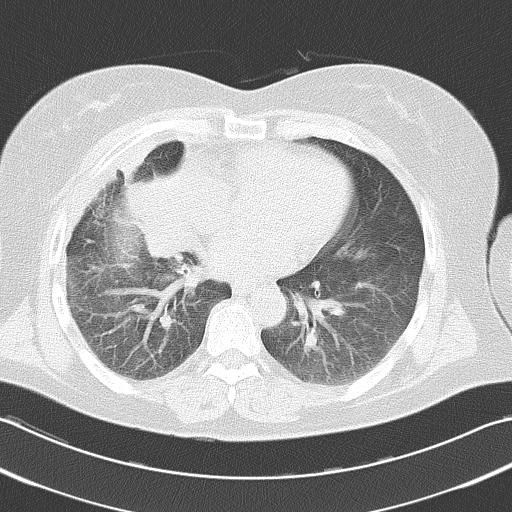
Chest CT, one axial slice. Slice 13 of 38 in the series (ordered by position). Reconstruction kernel B70f. Lung window (W 1500 / L -600 HU). 5 mm slice thickness. 512 × 512 image matrix, field of view 346 × 346 mm. Patient: female, 52 years. Case-level facts recorded for this patient, not image findings: clinical TNM (as recorded): T3 N1 M0.
Outlined on this slice (bounding box drawn by a radiologist):
- lung tumour (recorded histology: squamous cell carcinoma): bounding box <114,162,192,275> (left, top, right, bottom; pixels)